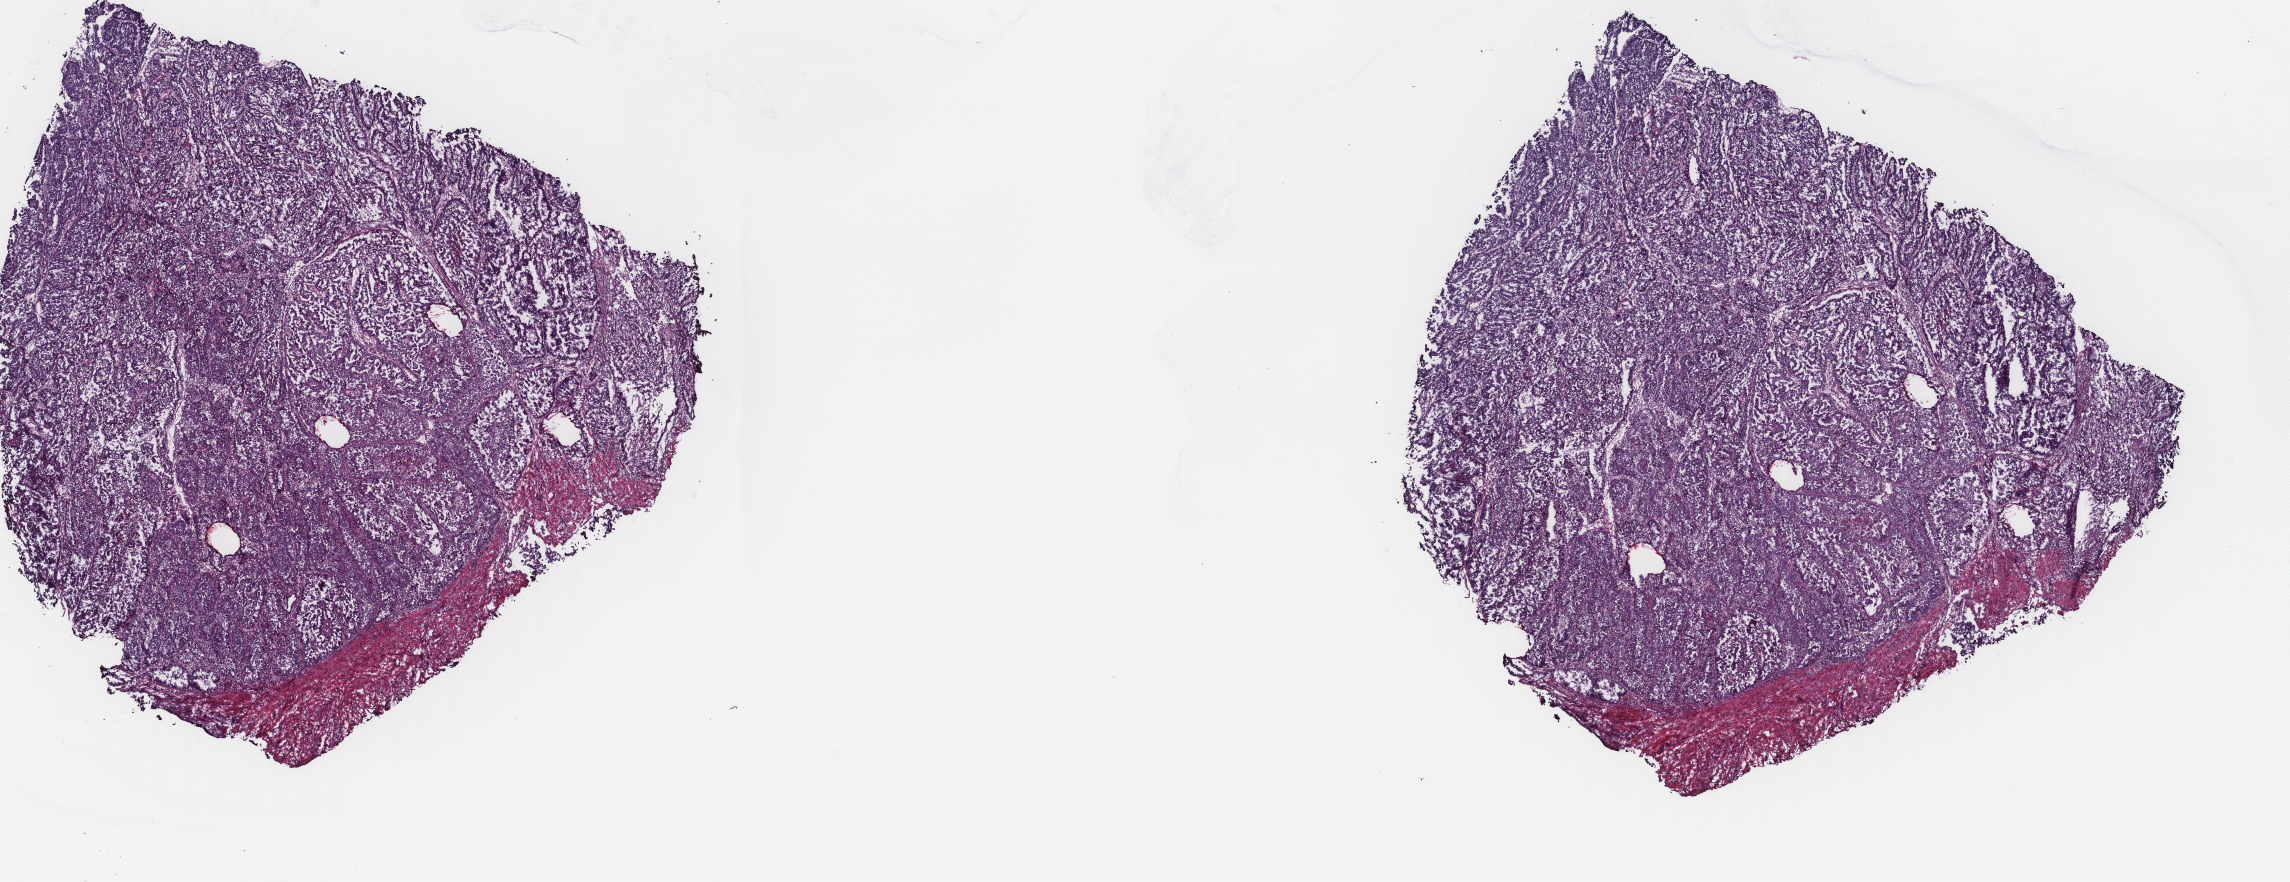
Whole-slide histology image, Hematoxylin and eosin (H&E) stained, low-resolution overview of the scanned area, about 18.2 x 7.0 mm. Frozen section from the top of the tissue portion. Sample: primary tumour, uterus. Female, age 61 years at initial diagnosis. Histologic grade: G3 (poorly differentiated). Slide review estimates, as recorded: tumour cells 60%, tumour nuclei 60%, normal cells 0%, stromal cells 30%, necrosis 10%. Inflammatory infiltration, as recorded: lymphocyte infiltration 60%, monocyte infiltration 10%, neutrophil infiltration 20%.
- histologic diagnosis: Serous cystadenocarcinoma, NOS (endometrium)
- FIGO stage: II